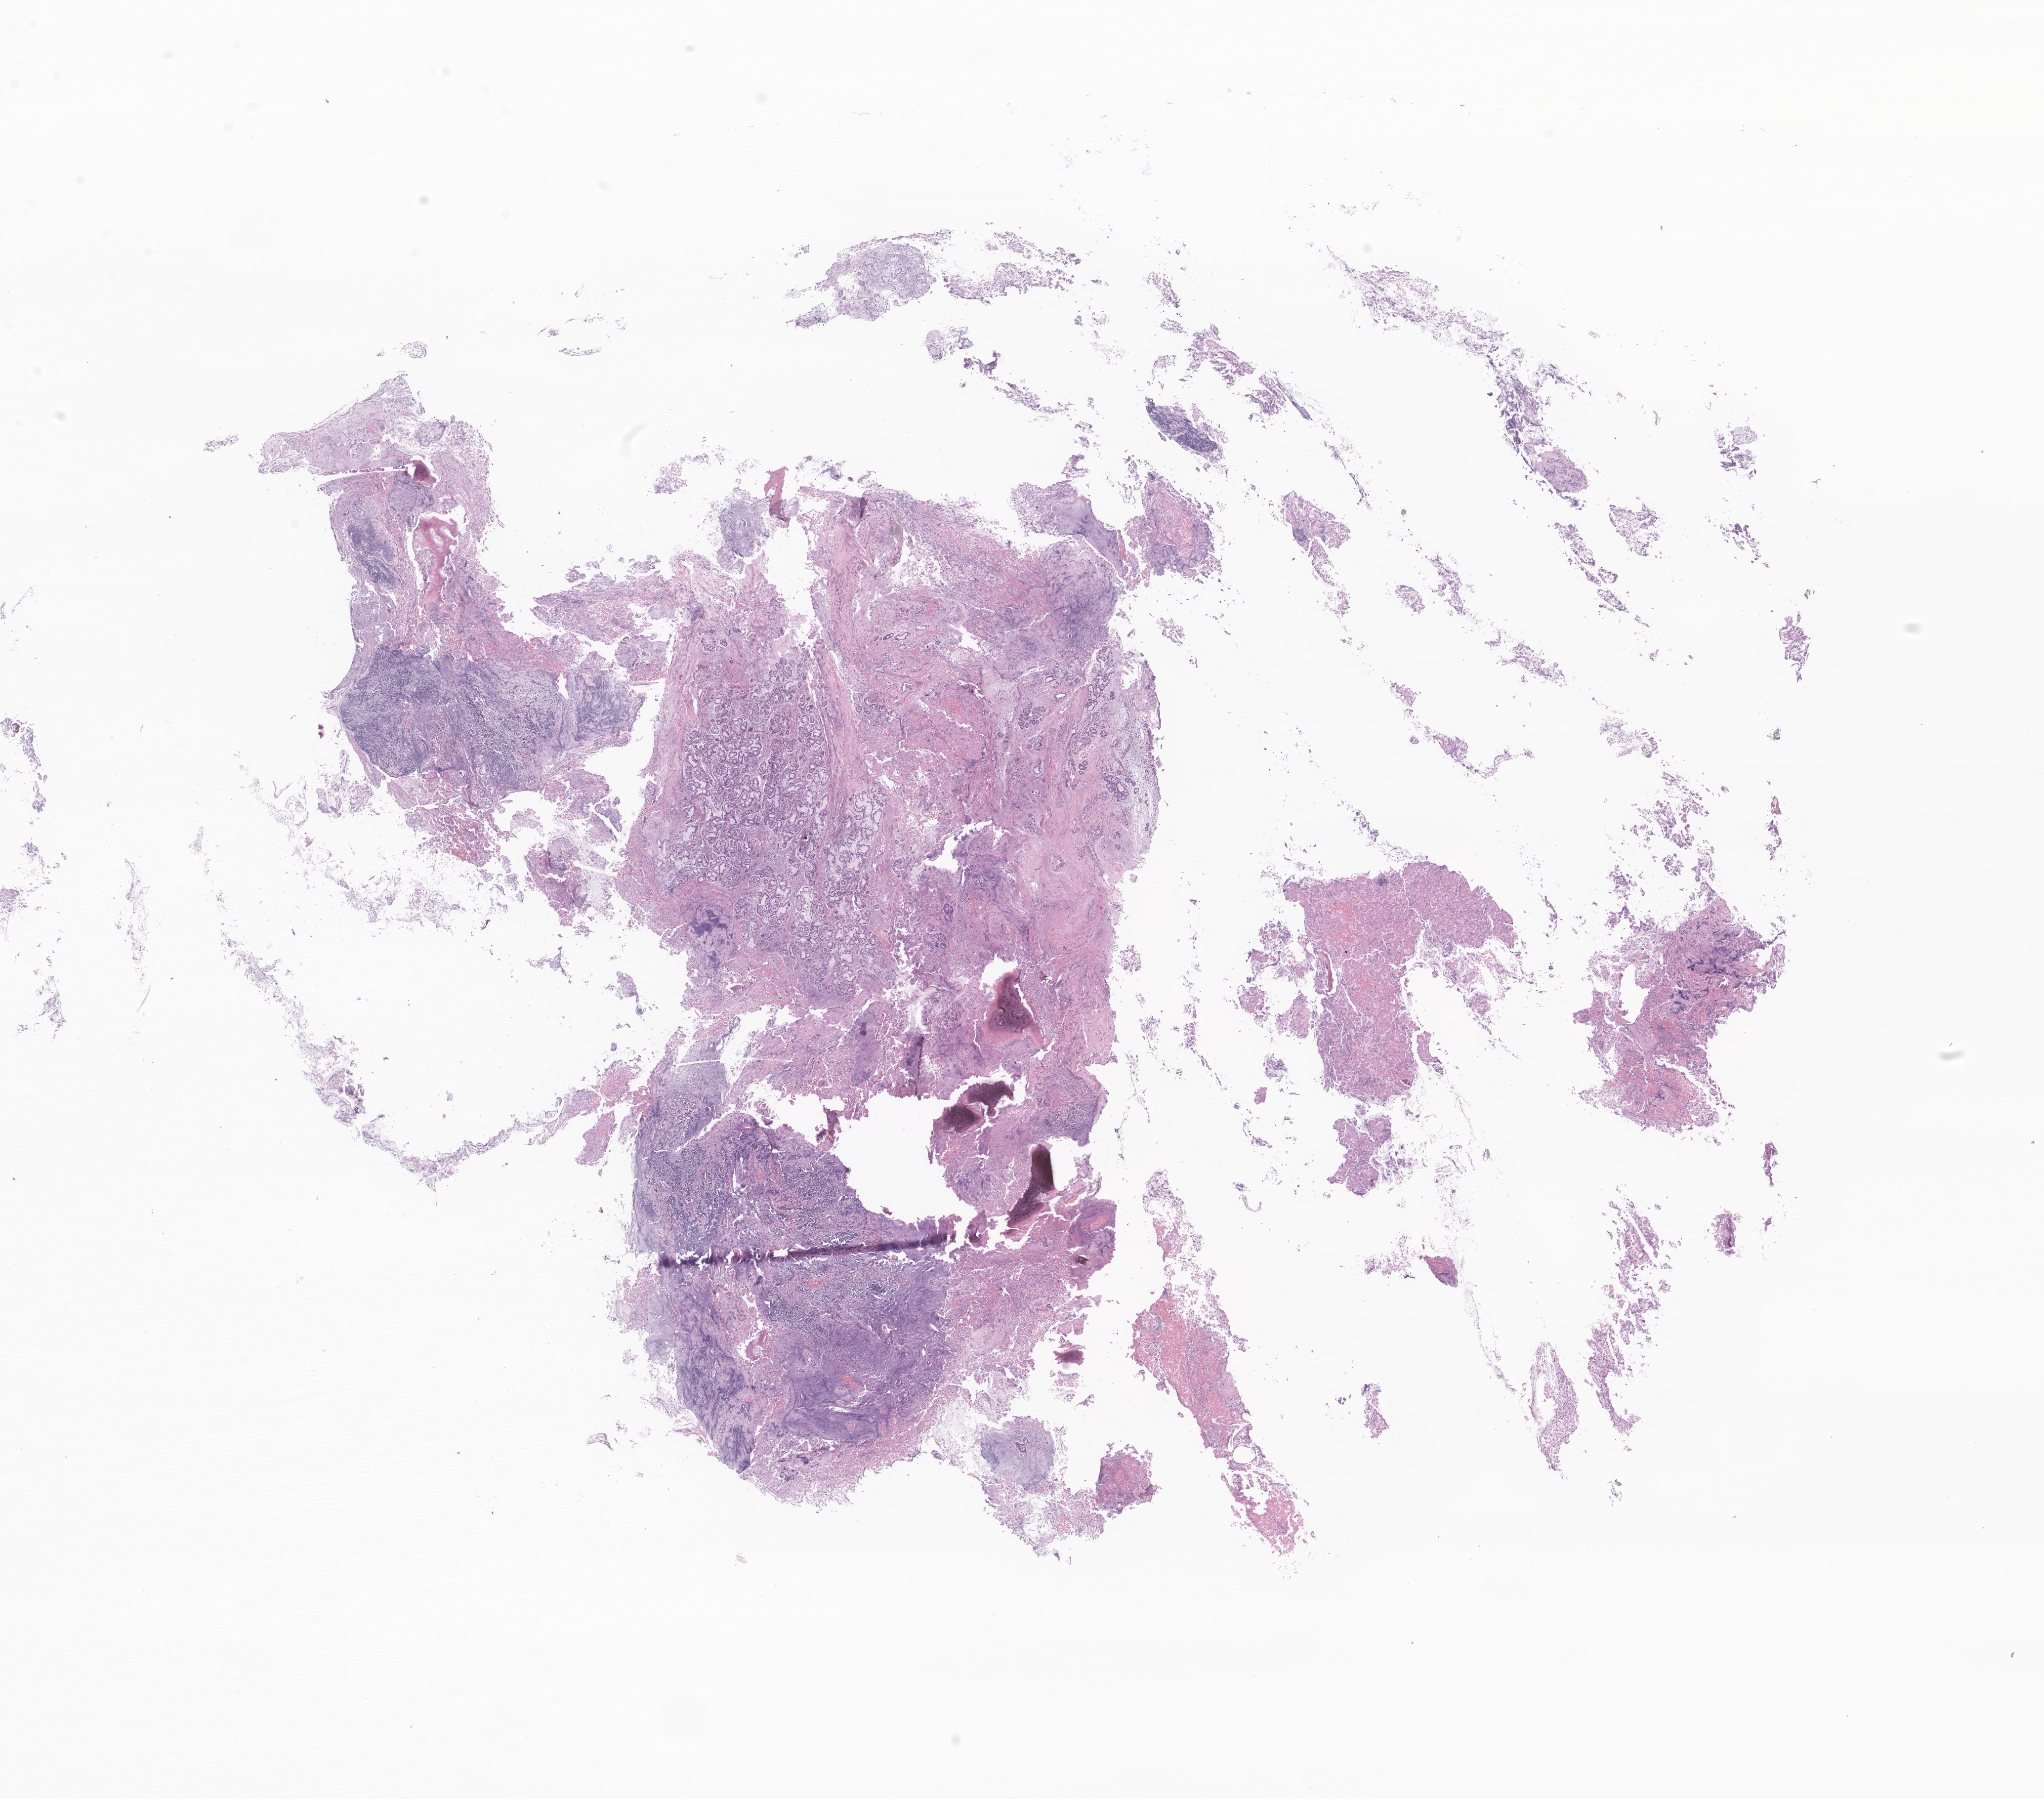
Digitized hematoxylin and eosin (H&E)-stained section of tumor tissue from the maxillary sinus, whole scanned area (about 17.4 x 15.3 mm) shown as a low-resolution overview, formalin-fixed paraffin-embedded section. Male patient, age 176 months (14 years 8 months).
* diagnosis (ICD-O-3 morphology term): Rhabdomyosarcoma, NOS